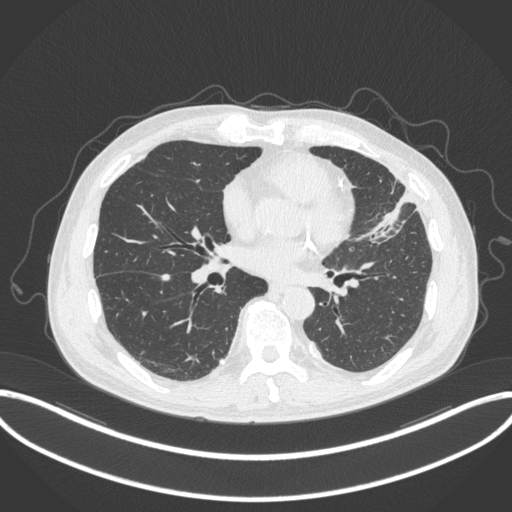
Chest CT, one axial slice; slice 149 of 382 in the series (ordered by position); reconstruction kernel B31f; lung window (W 1500 / L -600 HU); 512 × 512 image matrix, field of view 415 × 415 mm. Patient: male, 64 years. Case-level facts recorded for this patient, not image findings: clinical TNM (as recorded): T4 N1 M0.
Structures marked on this image (bounding box drawn by a radiologist):
- lung tumour (recorded histology: adenocarcinoma): bounding box <357,184,423,246> (left, top, right, bottom; pixels)